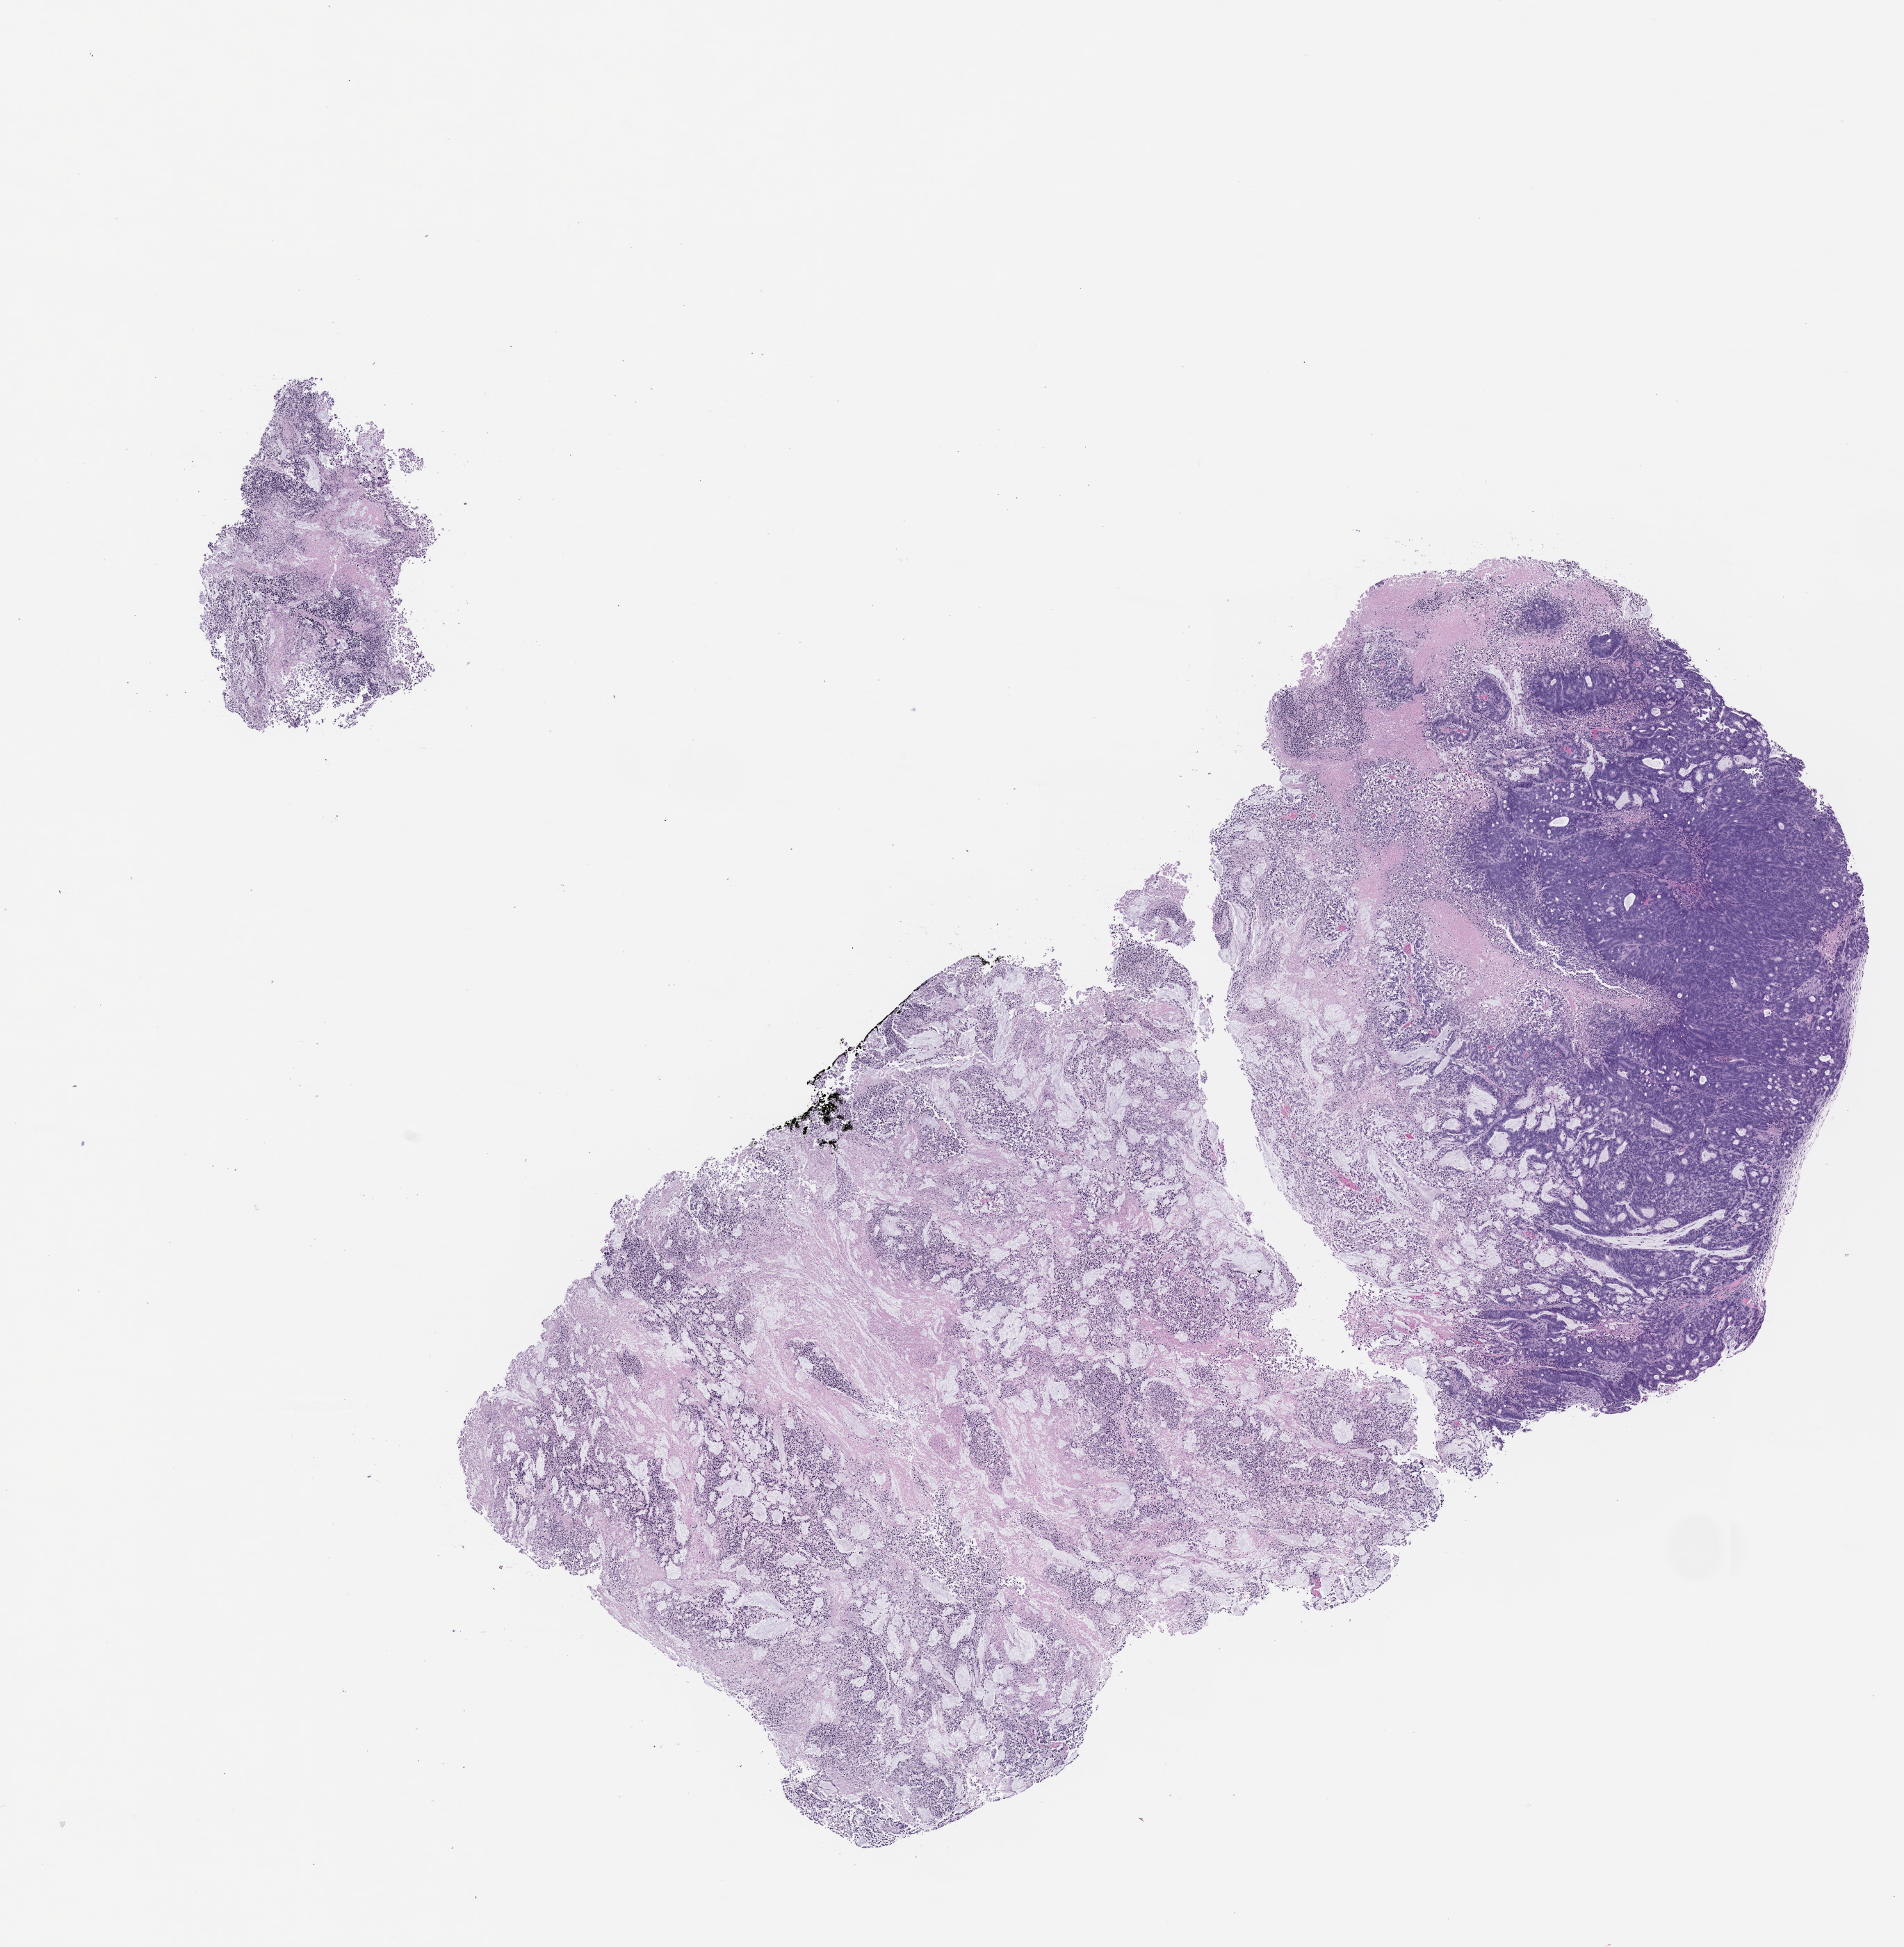
Haematoxylin and eosin whole-slide image of a patient-derived xenograft (PDX) tumor grown in a mouse, passage 1, whole scanned area (about 11.0 x 11.3 mm) shown as a low-resolution overview, formalin-fixed paraffin-embedded section, originating tumor site category: colon.
- originating patient diagnosis: Colon Adenocarcinoma